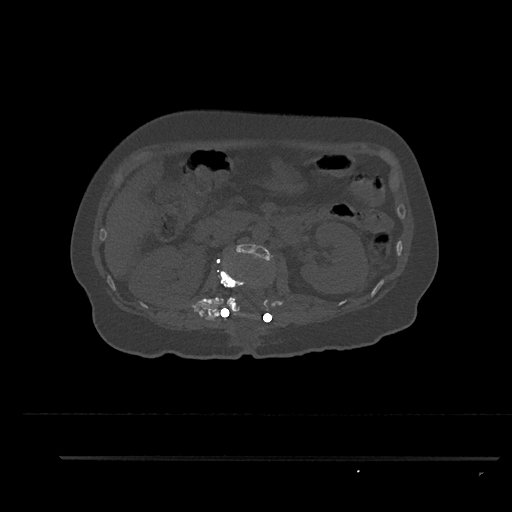
CT including the spine, one axial slice. Position 191 of 797 along the scan axis. 120 kVp. Bone window (W 1800 / L 400 HU). 0.5 mm slice thickness. 512 × 512 image matrix. Female patient, age 44 years. From the clinical record (not read from this slice): primary cancer: renal.
Structures marked on this image (semi-automatically segmented with operator editing):
- L1 vertebra: bounding box (x1, y1, x2, y2) in pixels: (217, 261, 244, 317)
- L2 vertebra: (226, 244, 272, 314)